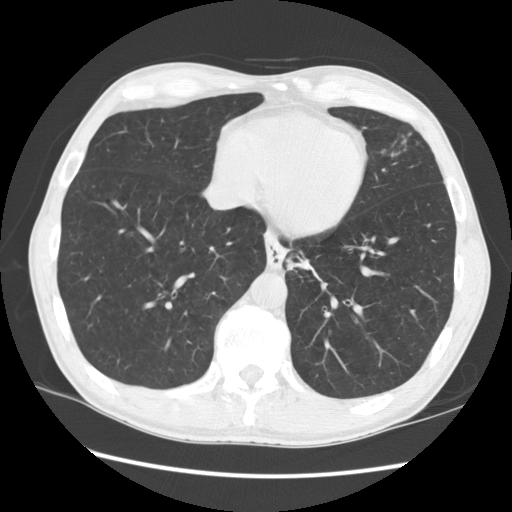
Axial slice from a low-dose chest CT screening exam, baseline annual screen, lung window (W 1500 / L -600 HU), 2.5 mm slice thickness, 512 × 512 image matrix. Male participant, aged 57 years at enrolment. Current smoker at enrolment.
Expert reader's lesion annotation, bounding box (x1, y1, x2, y2) in pixels: (269, 241, 336, 302). The screening reader recorded 2 non-calcified nodules or masses ≥4 mm on this exam (left lower lobe, lingula); which of them this box marks is not recorded. Lung cancer was diagnosed 95 days after this screen: squamous cell carcinoma, NOS, left lower lobe, moderately differentiated (G2), stage IB (AJCC 6th edition), 35 mm at pathology.